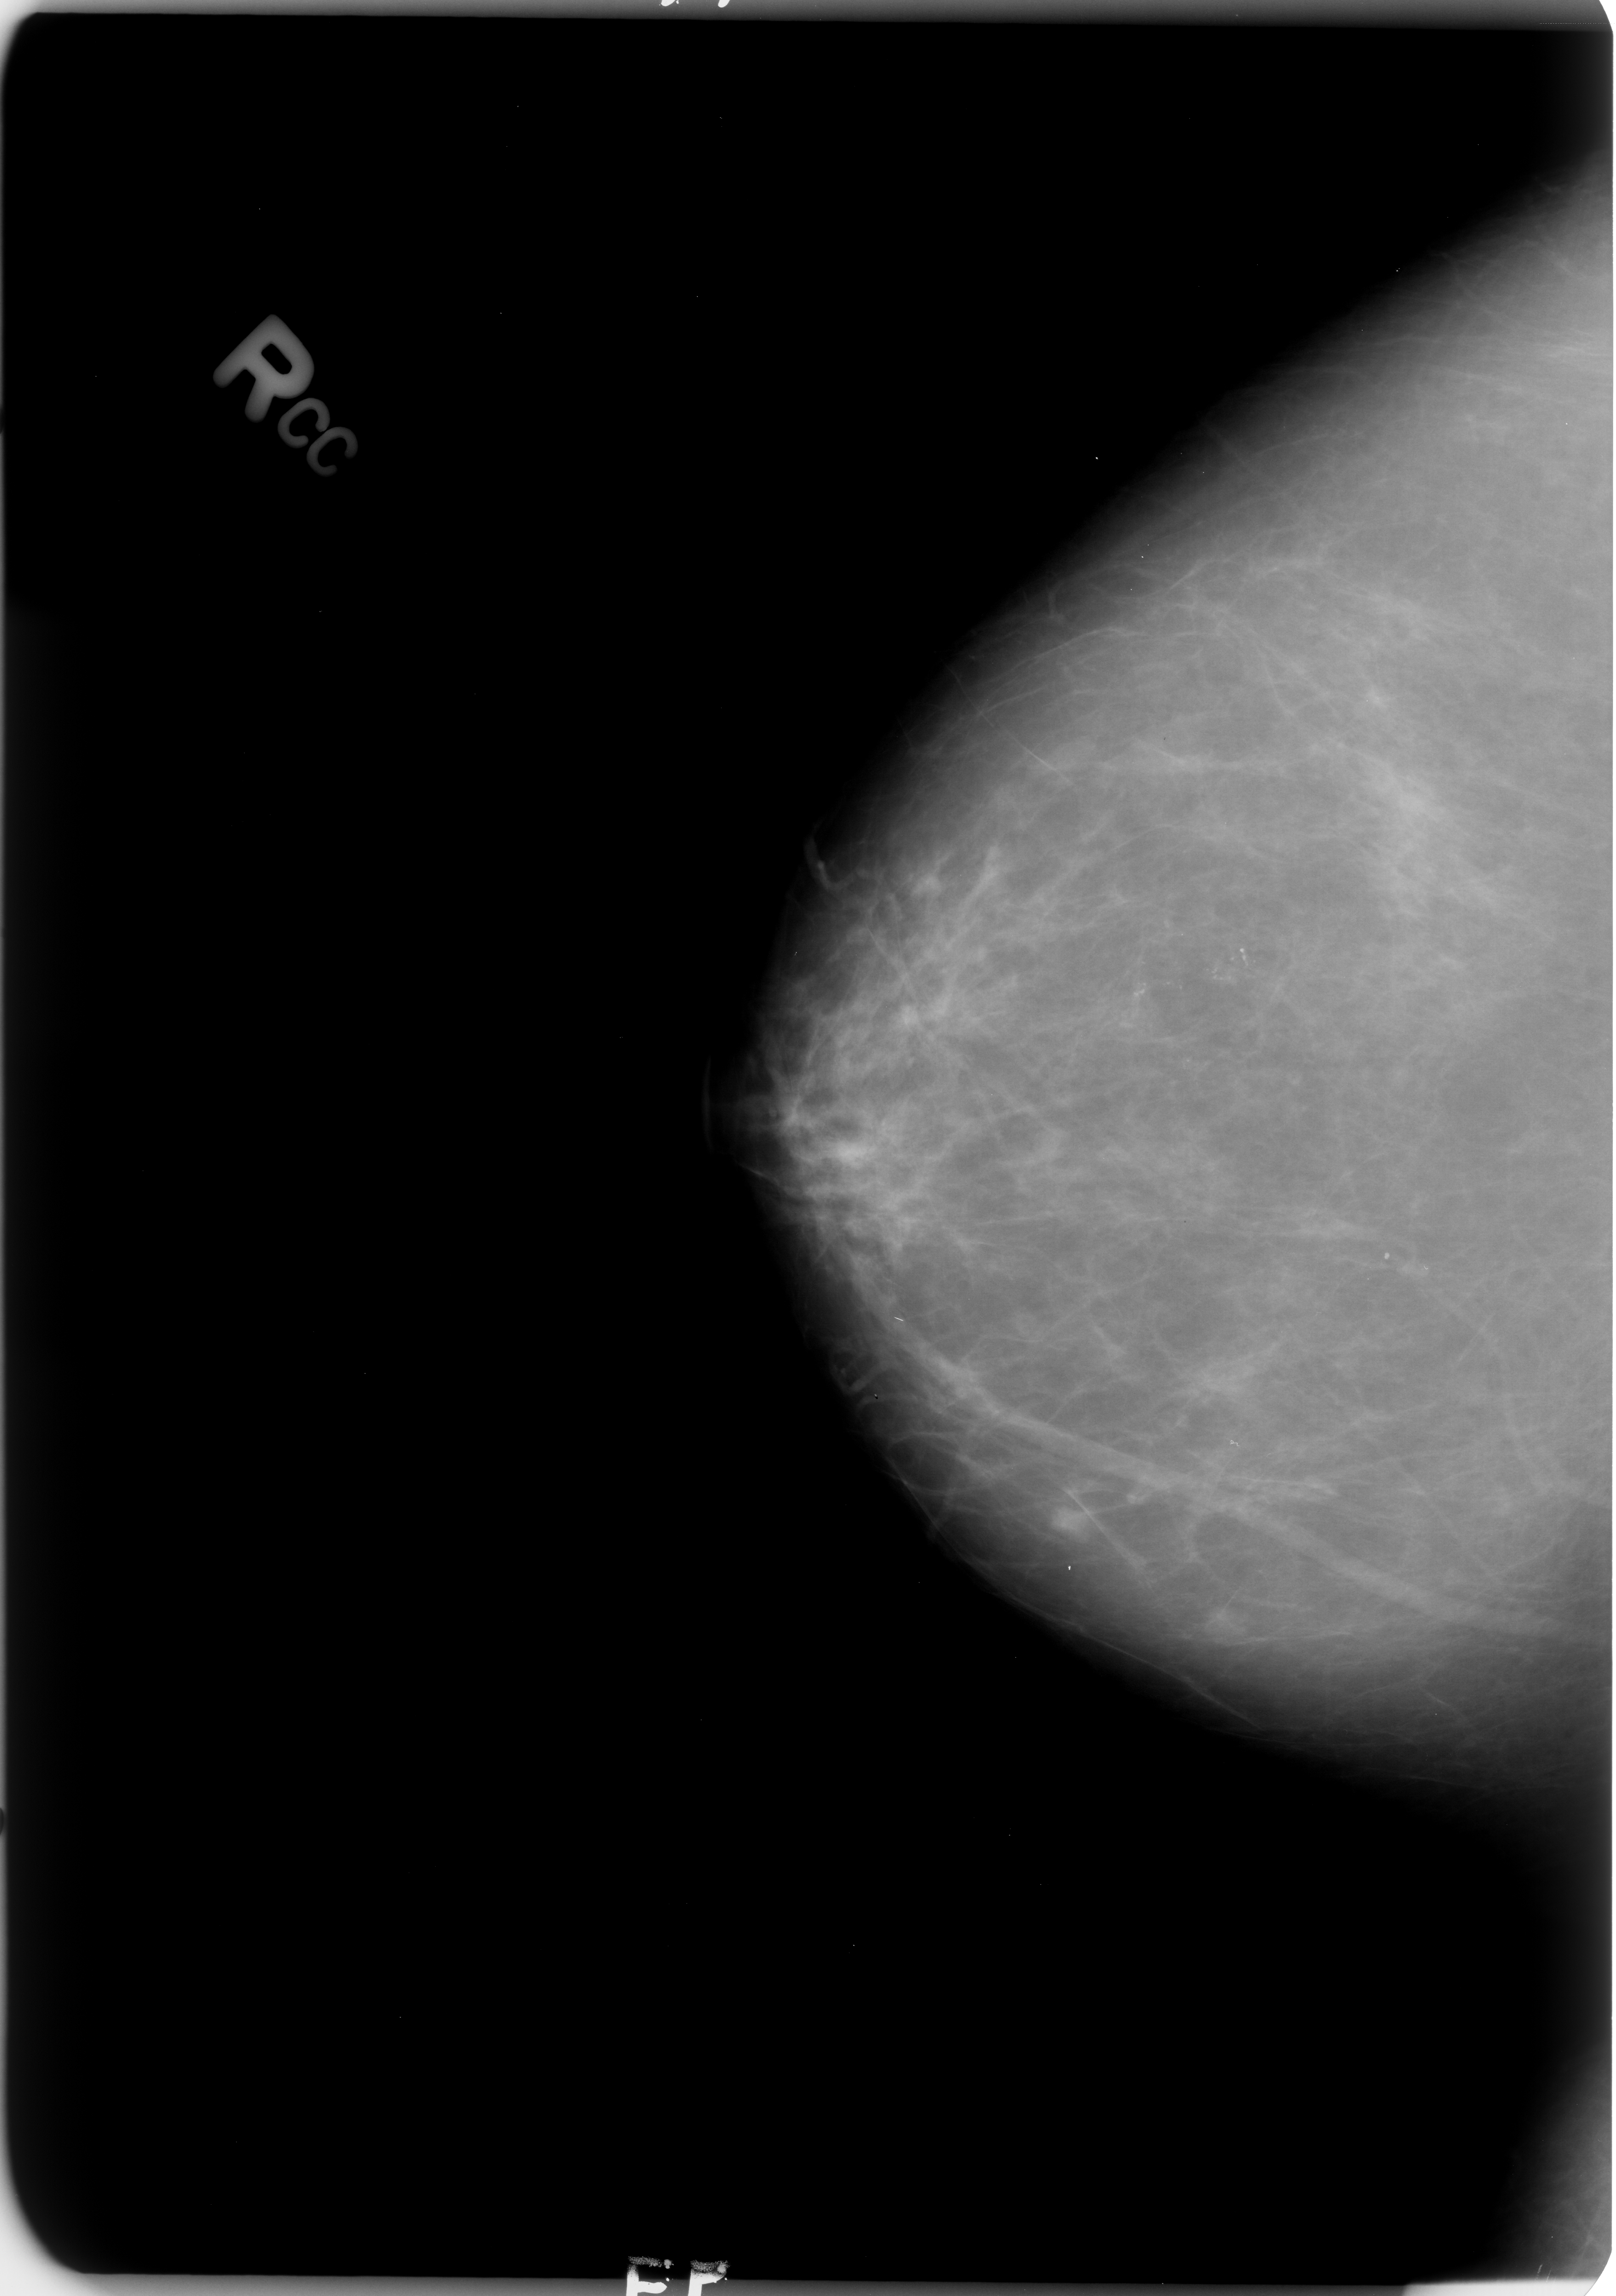
Mammogram (digitized film). Right breast. Craniocaudal (CC) view. Breast composition: scattered fibroglandular densities (BI-RADS density category 2 of 4). 1616 × 2296 image matrix.
Marked abnormalities (boxes around the expert regions of interest):
- Finding 1 of 2: calcifications, morphology pleomorphic, distribution clustered; BI-RADS assessment category 4; subtlety rating 3 on a 1 (subtle) to 5 (obvious) scale; pathology result (as recorded, not read from the image): malignant: bounding box <1115,976,1166,1034> (left, top, right, bottom; pixels)
- Finding 2 of 2: calcifications, morphology pleomorphic, distribution clustered; BI-RADS assessment category 4; subtlety rating 3 on a 1 (subtle) to 5 (obvious) scale; pathology (as recorded): malignant: <1197,932,1264,1002>